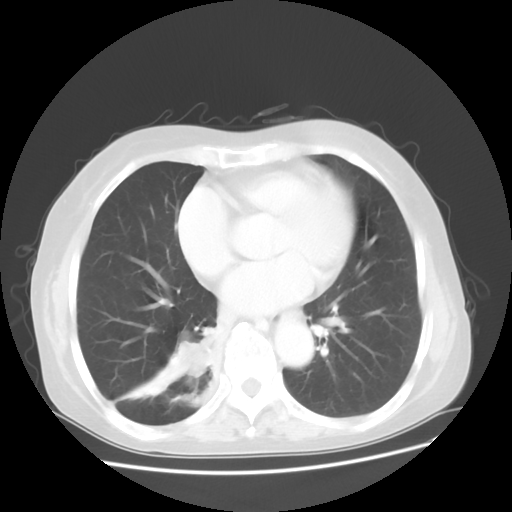
Chest CT, one axial slice. Position 18 of 48 along the scan axis. Reconstruction kernel STANDARD. Lung window (W 1500 / L -600 HU). 5 mm slice thickness. 512 × 512 image matrix, field of view 360 × 360 mm. Patient: female, 63 years. From the clinical record (not read from this slice): clinical TNM (as recorded): T2 N3 M1b; histopathological grade: G3.
Outlined on this slice (rectangle marked by the reading radiologist):
- lung tumour (recorded histology: small cell carcinoma): bounding box <174,333,228,392> (left, top, right, bottom; pixels)